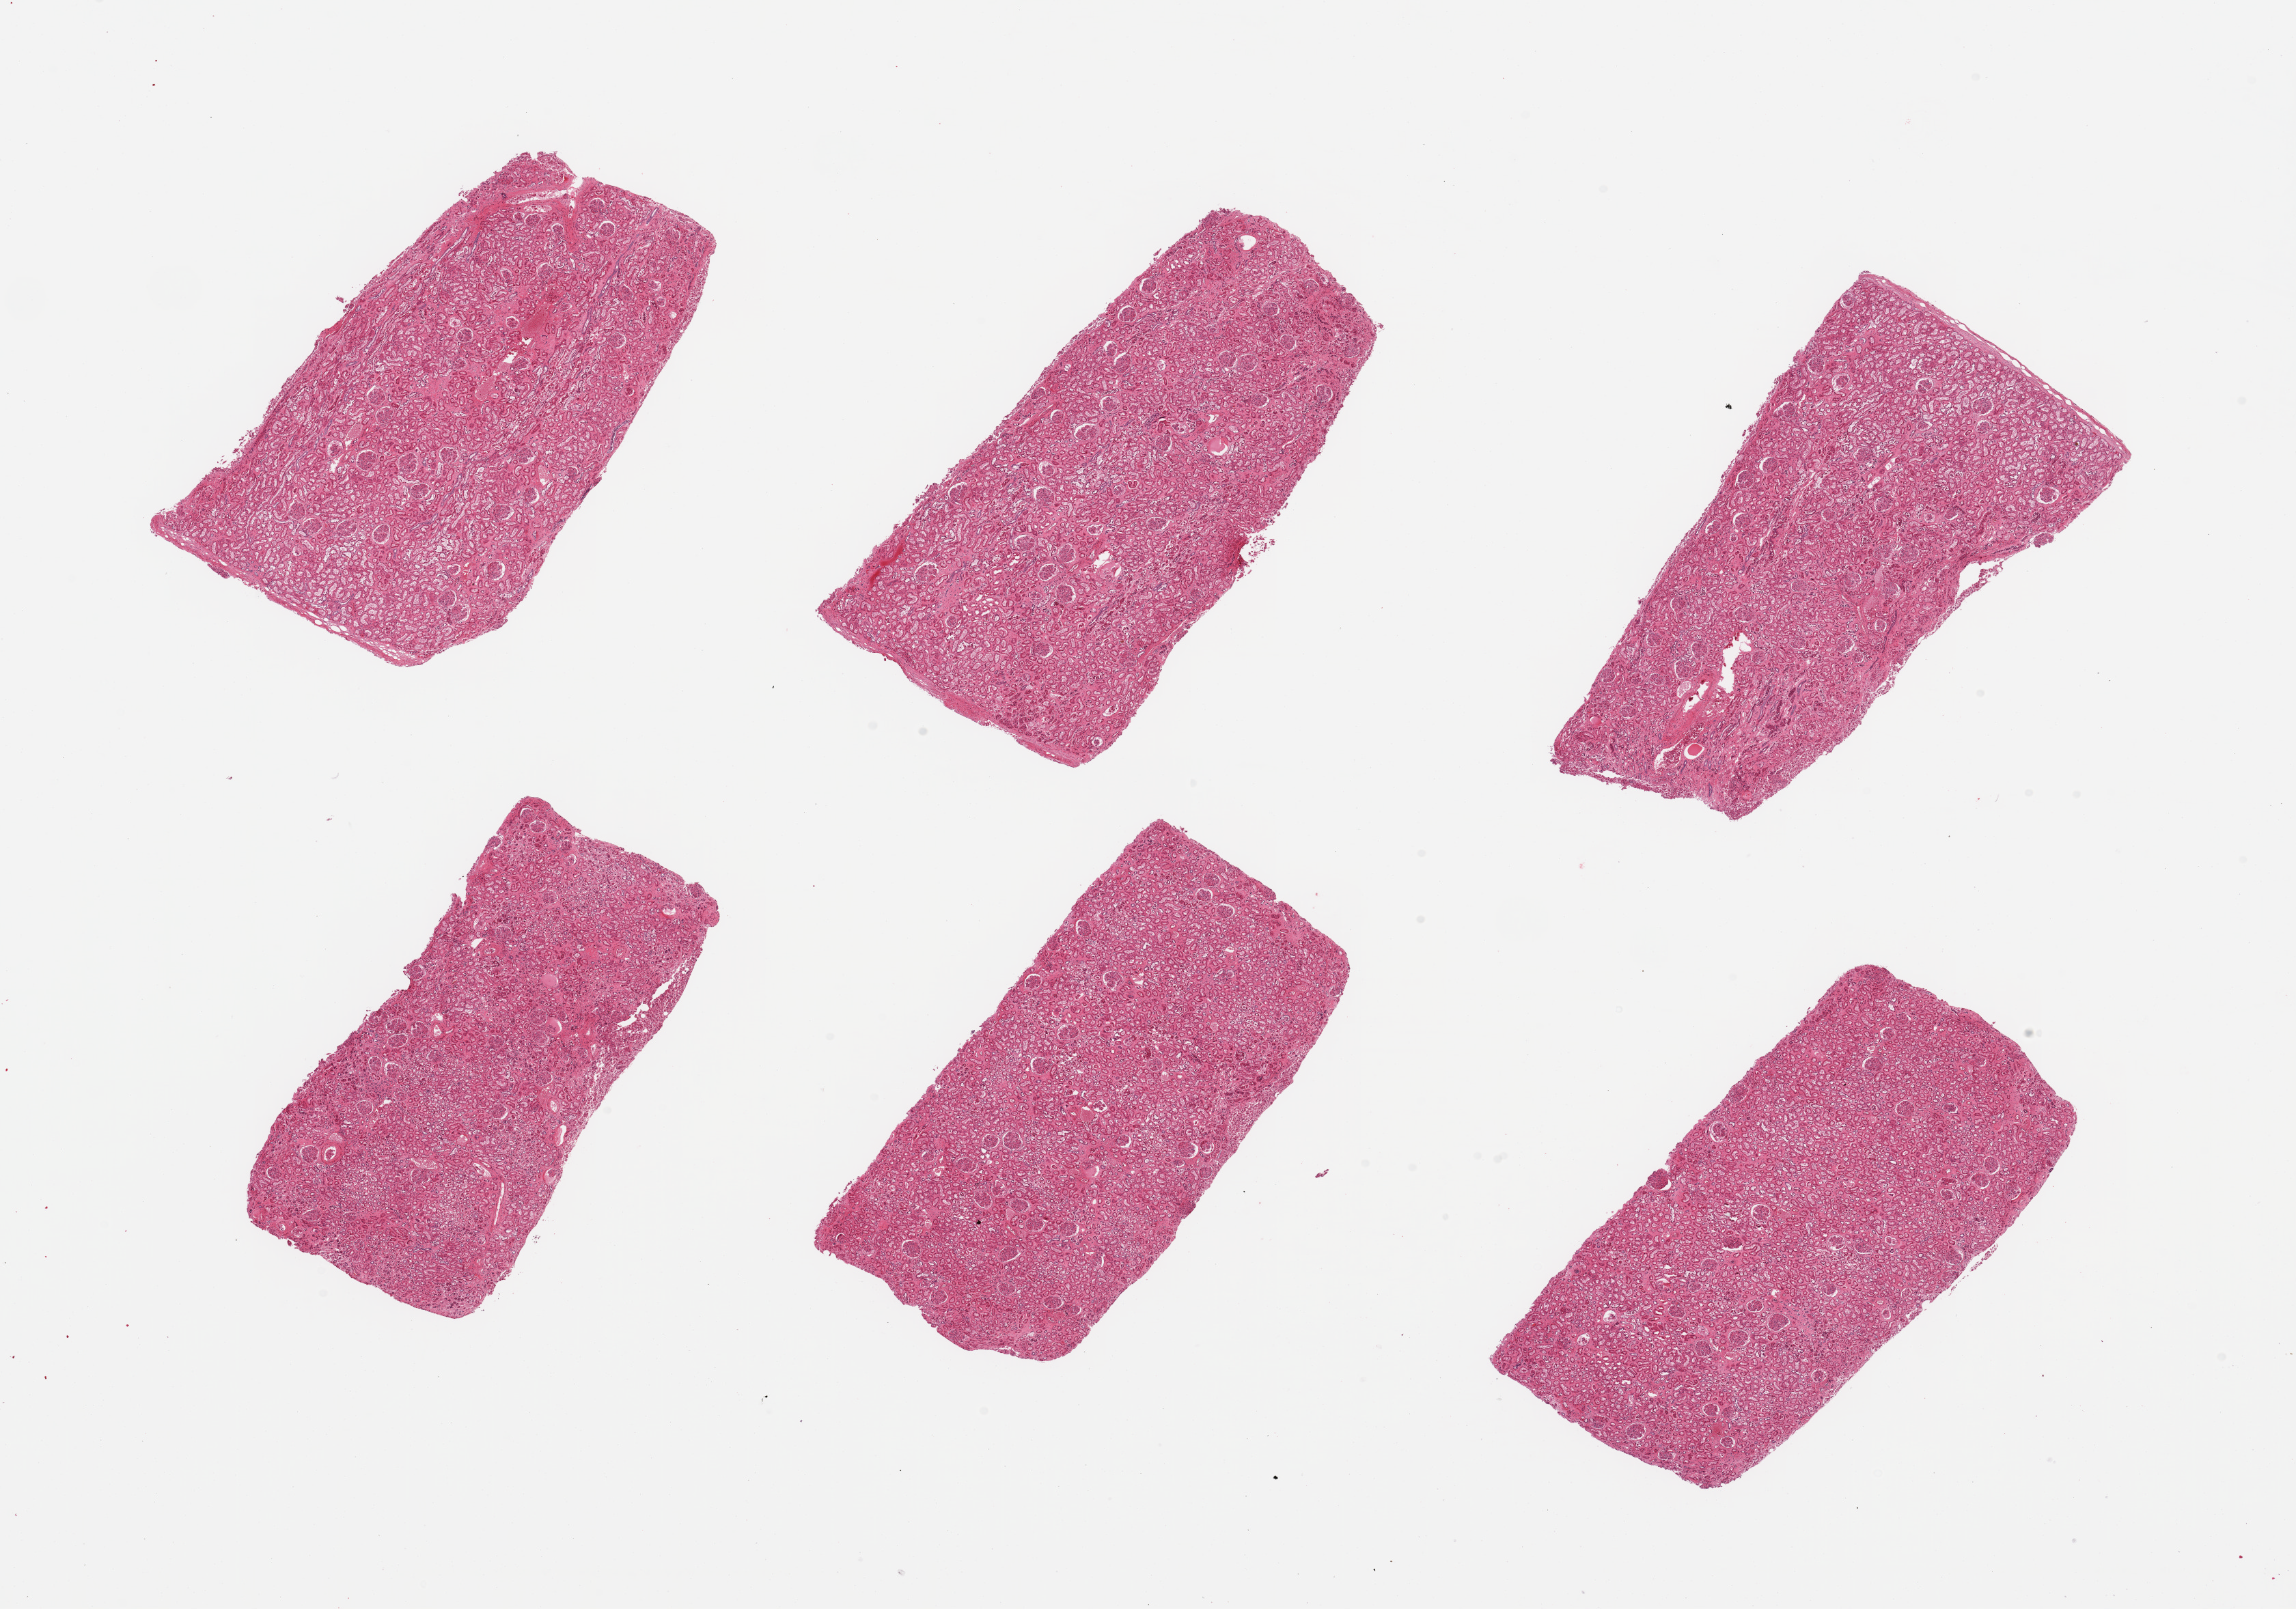
Digitized haematoxylin and eosin-stained section, shown as a low-resolution overview of the whole scanned area (about 26.6 x 18.6 mm), PAXgene-fixed, paraffin-embedded tissue, target tissue: renal cortex, donor tissue sample. Donor: male.
Pathologist's review note for this sample: 6 pieces, glomeruli present.